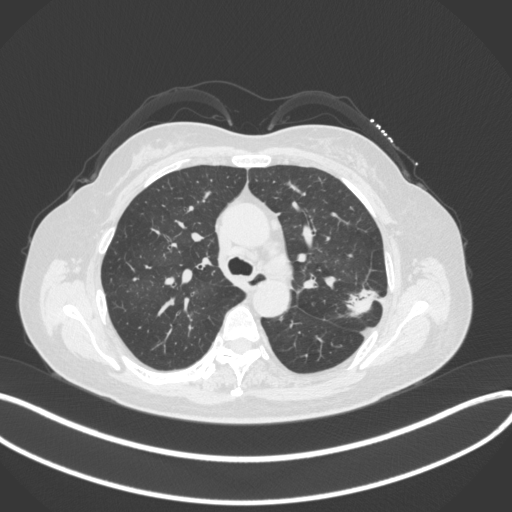
Chest CT, one axial slice; position 230 of 330 along the scan axis; reconstruction kernel B31f; 120 kVp; lung window (W 1500 / L -600 HU); 512 × 512 image matrix, field of view 400 × 400 mm. Female patient, age 60 years. Case-level facts recorded for this patient, not image findings: clinical TNM (as recorded): T1c N0 M0.
Annotated regions visible in this slice (rectangle marked by the reading radiologist):
- lung tumour (recorded histology: adenocarcinoma): box from (x=344, y=282) to (x=378, y=320) px